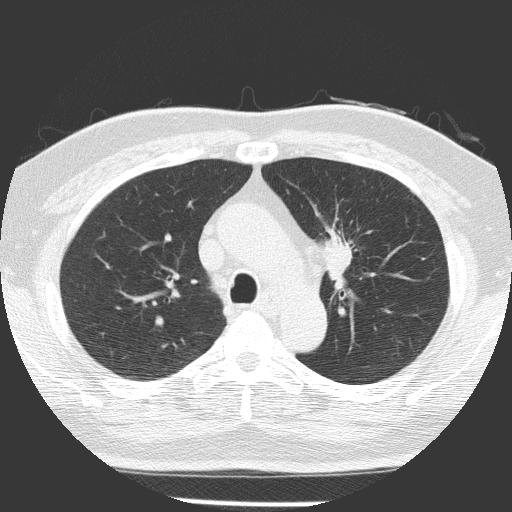
Low-dose screening chest CT, axial slice; baseline screening round; lung window (W 1500 / L -600 HU); lung (sharp) reconstruction kernel (FC51); 512 × 512 image matrix, field of view 309 × 309 mm. Male, age 70 years at enrolment. Current smoker at enrolment.
- Expert reader's lesion annotation, bounding box [x1, y1, x2, y2] px = [299, 224, 371, 300].
- The screening reader recorded 3 non-calcified nodules or masses ≥4 mm on this exam (left upper lobe, left lower lobe, left upper lobe); which of them this box marks is not recorded.